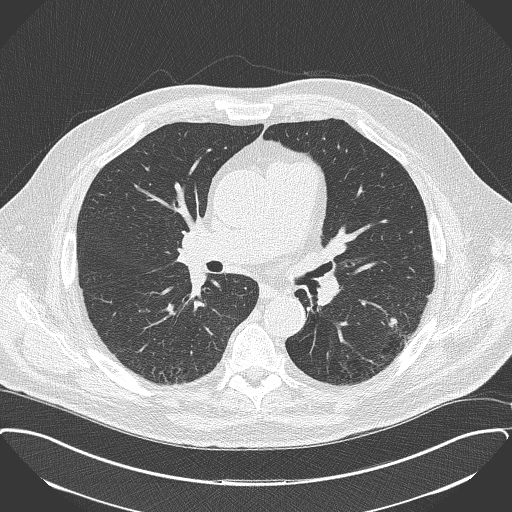
Chest CT (low-dose screening protocol), one axial image, second annual screen, lung window (W 1500 / L -600 HU), 2 mm slice thickness, 120 kVp. Male participant, aged 68 years at enrolment. Former smoker at enrolment.
• Expert reader's lesion annotation, bounding box [x1, y1, x2, y2] px = [375, 293, 433, 346].
• The screening reader recorded 2 non-calcified nodules or masses ≥4 mm on this exam; which of them this box marks is not recorded.
• Official screen result: positive, other.
• Later outcome: lung cancer diagnosed 126 days after this screen — adenocarcinoma, NOS, left lower lobe, poorly differentiated (G3), stage IB (AJCC 6th edition), 17 mm at pathology.